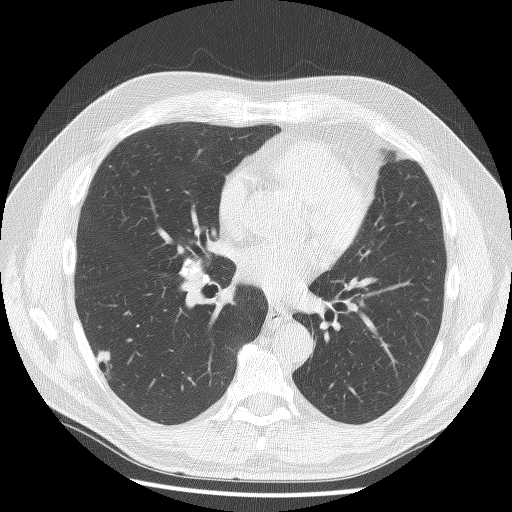
Low-dose screening chest CT, axial slice; baseline annual screen; lung window (W 1500 / L -600 HU); 2.5 mm slice thickness; lung (sharp) reconstruction kernel (BONE); slice 91 of 179 in the series. Male participant, aged 61 years at enrolment. Former smoker at enrolment.
- Expert-annotated lung lesion, bounding box (x1, y1, x2, y2) in pixels: (79, 338, 129, 389).
- Screening reader's record for this exam (one nodule recorded; not confirmed to be the boxed lesion): non-calcified nodule or mass ≥4 mm, right lower lobe, 10 × 8 mm, spiculated (stellate) margins, soft tissue attenuation.
- Participant outcome: lung cancer diagnosed 407 days after this screen — adenosquamous carcinoma, right lower lobe, poorly differentiated (G3), stage IV (AJCC 6th edition), 45 mm at pathology.